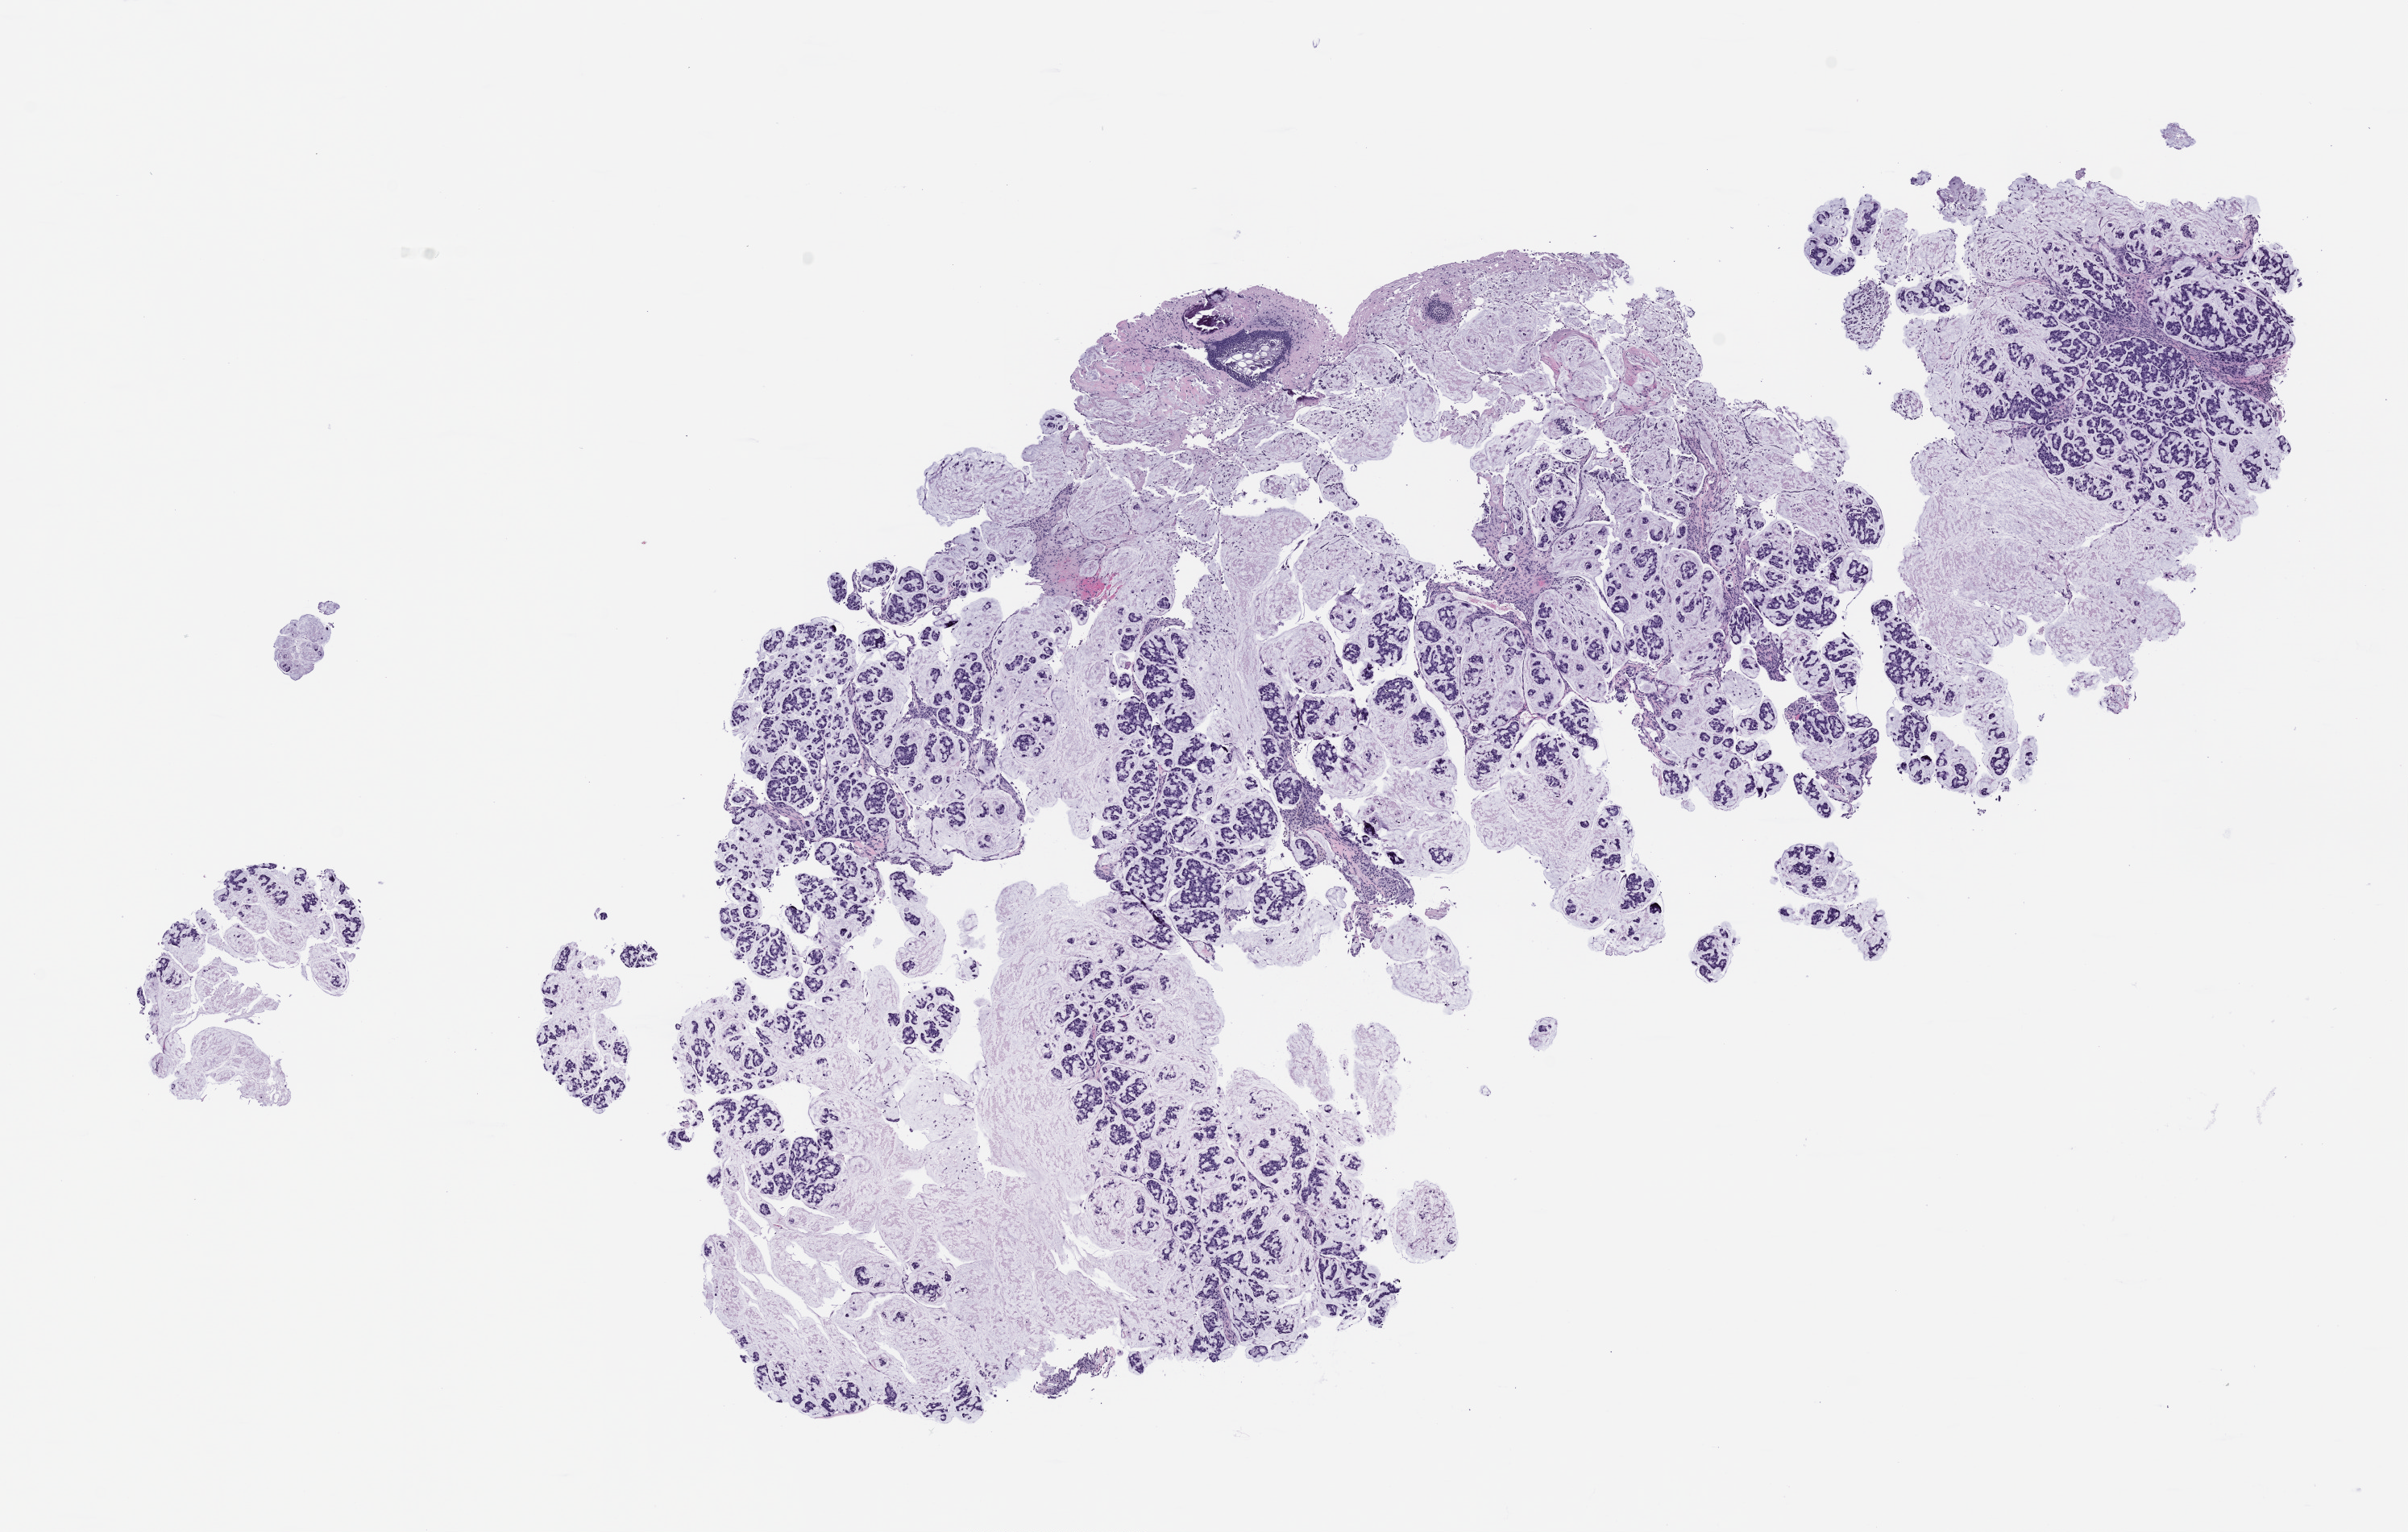
H&E whole-slide image of a patient-derived xenograft (PDX) tumor grown in a mouse, passage 2, a low-resolution overview of the entire scanned area, about 12.0 x 7.6 mm, formalin-fixed paraffin-embedded section, tumor site category: colon.
• originating patient diagnosis: Colon Adenocarcinoma